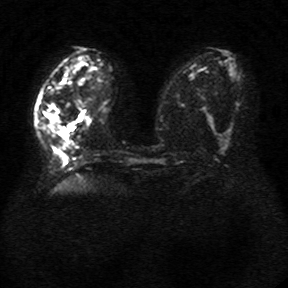
Breast MRI, one axial slice. Position 15 of 34 along the scan axis. Diffusion-weighted series; image 2 of 4 stored at this slice position (different b-values; order by instance number). 1.5 T. 288 × 288 image matrix, field of view 340 × 340 mm. Female patient.
Annotated regions visible in this slice (outlined manually by an expert reader):
- tumour on diffusion-weighted imaging: bounding box (x1, y1, x2, y2) in pixels: (42, 105, 69, 138)